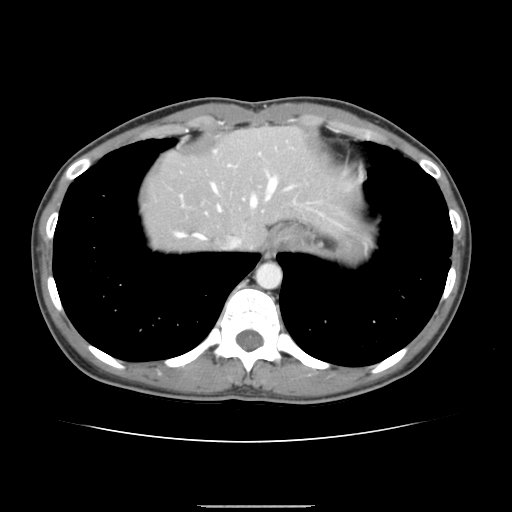
Contrast-enhanced abdominal CT, one axial slice. Slice 125 of 150 in the series (ordered by position). 120 kVp. Intravenous contrast given. Soft-tissue window (W 400 / L 40 HU). 2.5 mm slice thickness. 512 × 512 image matrix, field of view 324 × 324 mm. Female patient, age 32 years. From the clinical record (not read from this slice): diagnosis: colorectal cancer liver metastases, imaged before liver resection; multiple liver metastases: yes; largest metastasis: 0.7 cm; chemotherapy before resection: yes.
Structures marked on this image (expert manual segmentation):
- hepatic veins: bounding box <176,175,291,248> (left, top, right, bottom; pixels)
- liver: <144,127,345,251>
- planned liver remnant (the part of the liver to remain after resection): <144,128,345,248>
- portal vein (with intrahepatic branches): <229,153,260,166>